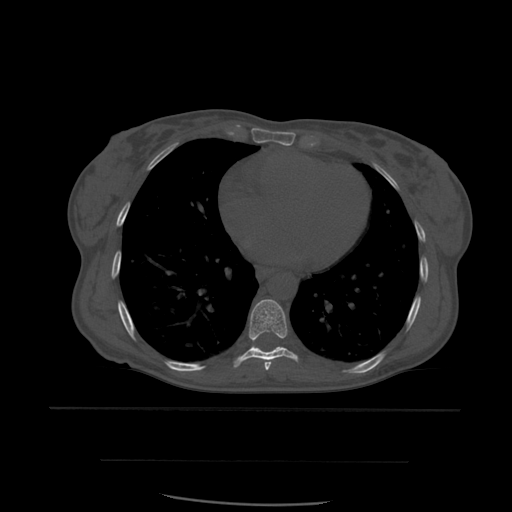
CT including the spine, one axial slice. Position 356 of 574 along the scan axis. Bone window (W 1800 / L 400 HU). 1.25 mm slice thickness. 512 × 512 image matrix, field of view 392 × 392 mm. Patient age 48 years. Case-level facts recorded for this patient, not image findings: primary cancer: lung; vertebrae with lytic lesions (as recorded): T11.
Structures marked on this image (semi-automatically segmented with operator editing):
- T7 vertebra: bounding box [x1, y1, x2, y2] px = [265, 362, 271, 371]
- T8 vertebra: [233, 299, 299, 368]
- T9 vertebra: [253, 346, 259, 349]